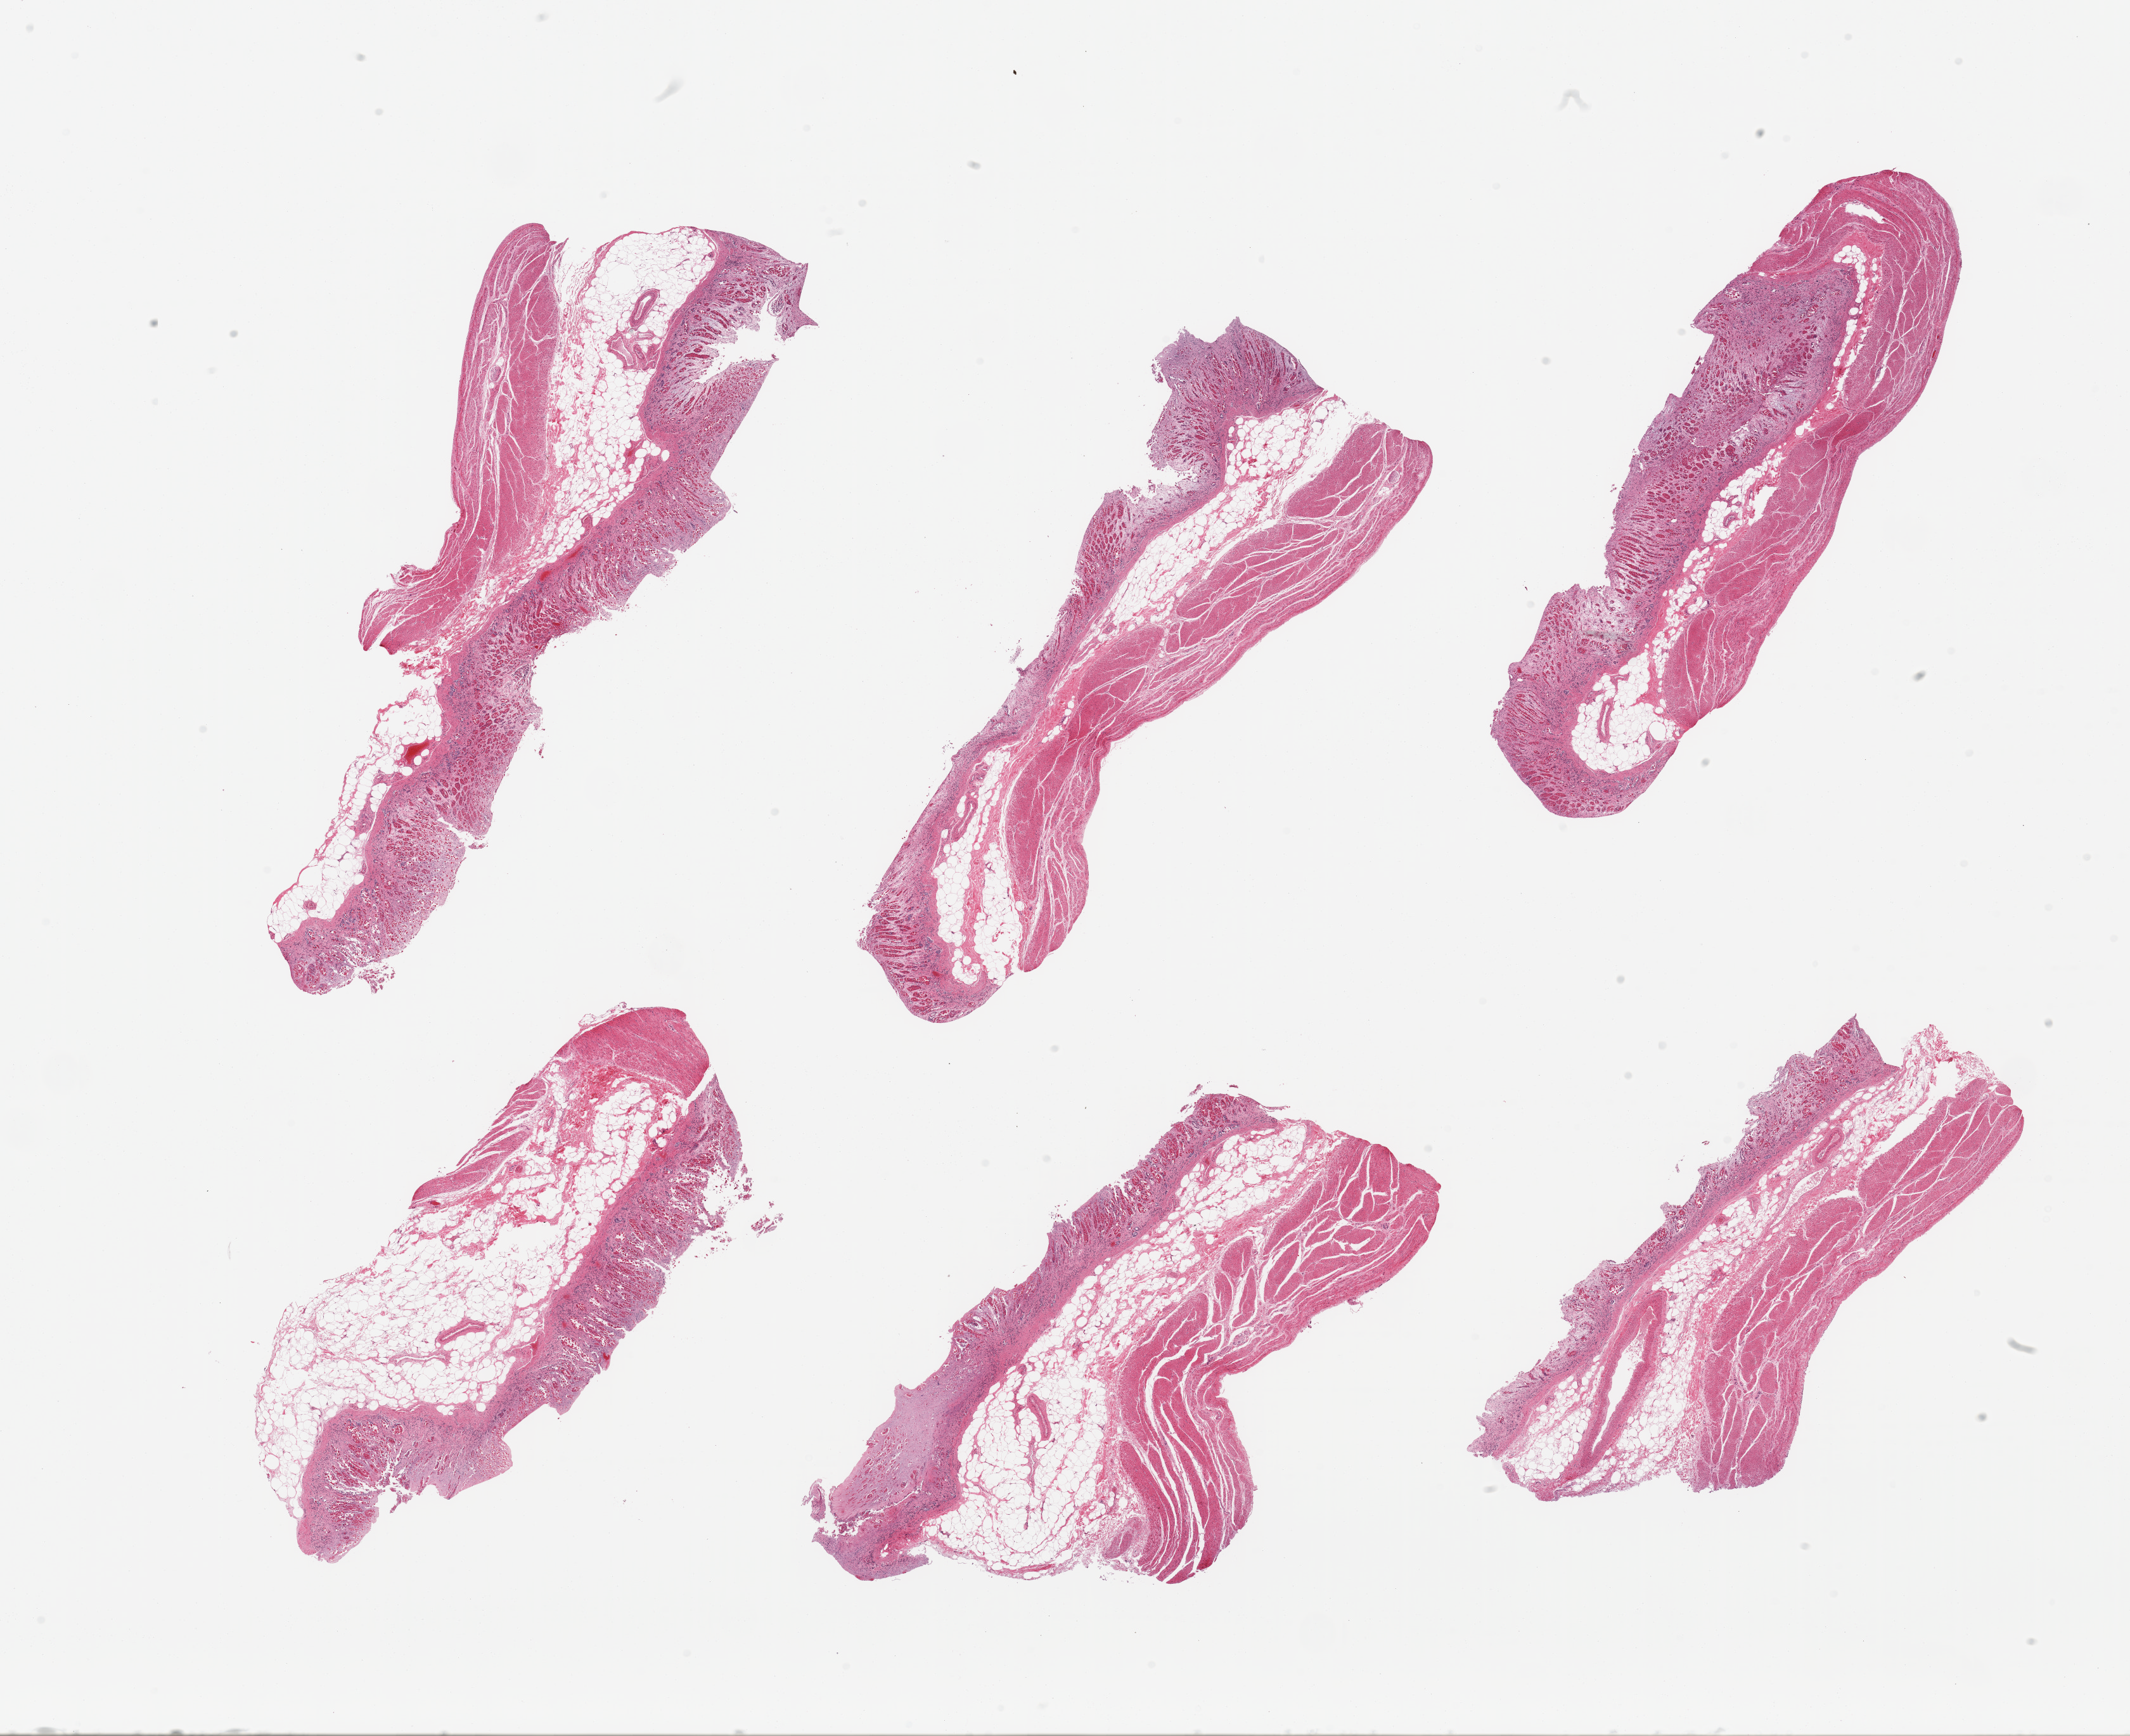
Whole-slide image, H&E stain, brightfield — whole scanned area (about 26.6 x 21.7 mm) shown as a low-resolution overview. PAXgene-fixed, paraffin-embedded tissue. Sampled site (target tissue): stomach. Tissue donor sample.
Review note (as recorded): 6 pieces target muscosa up to ~1.2mm, ~50% thickenss, but with advanced autolysis/soughing.